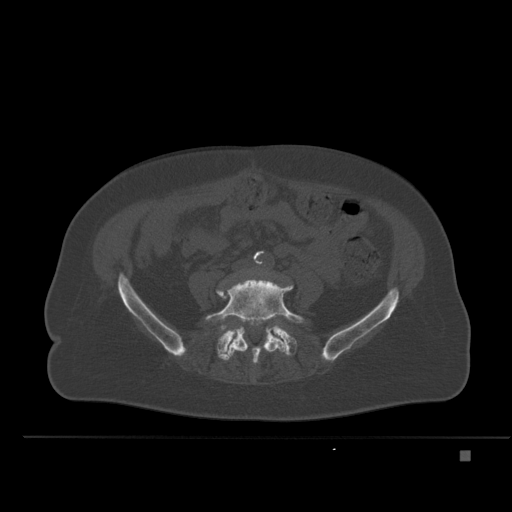
CT including the spine, one axial slice; bone window (W 1800 / L 400 HU); 512 × 512 image matrix, field of view 422 × 422 mm. Female patient, age 74 years. Case-level facts recorded for this patient, not image findings: primary cancer: colon.
Structures marked on this image (semi-automatic segmentation, software-assisted and operator-edited):
- L4 vertebra: bounding box (x1, y1, x2, y2) in pixels: (216, 274, 260, 294)
- L5 vertebra: (205, 278, 305, 365)